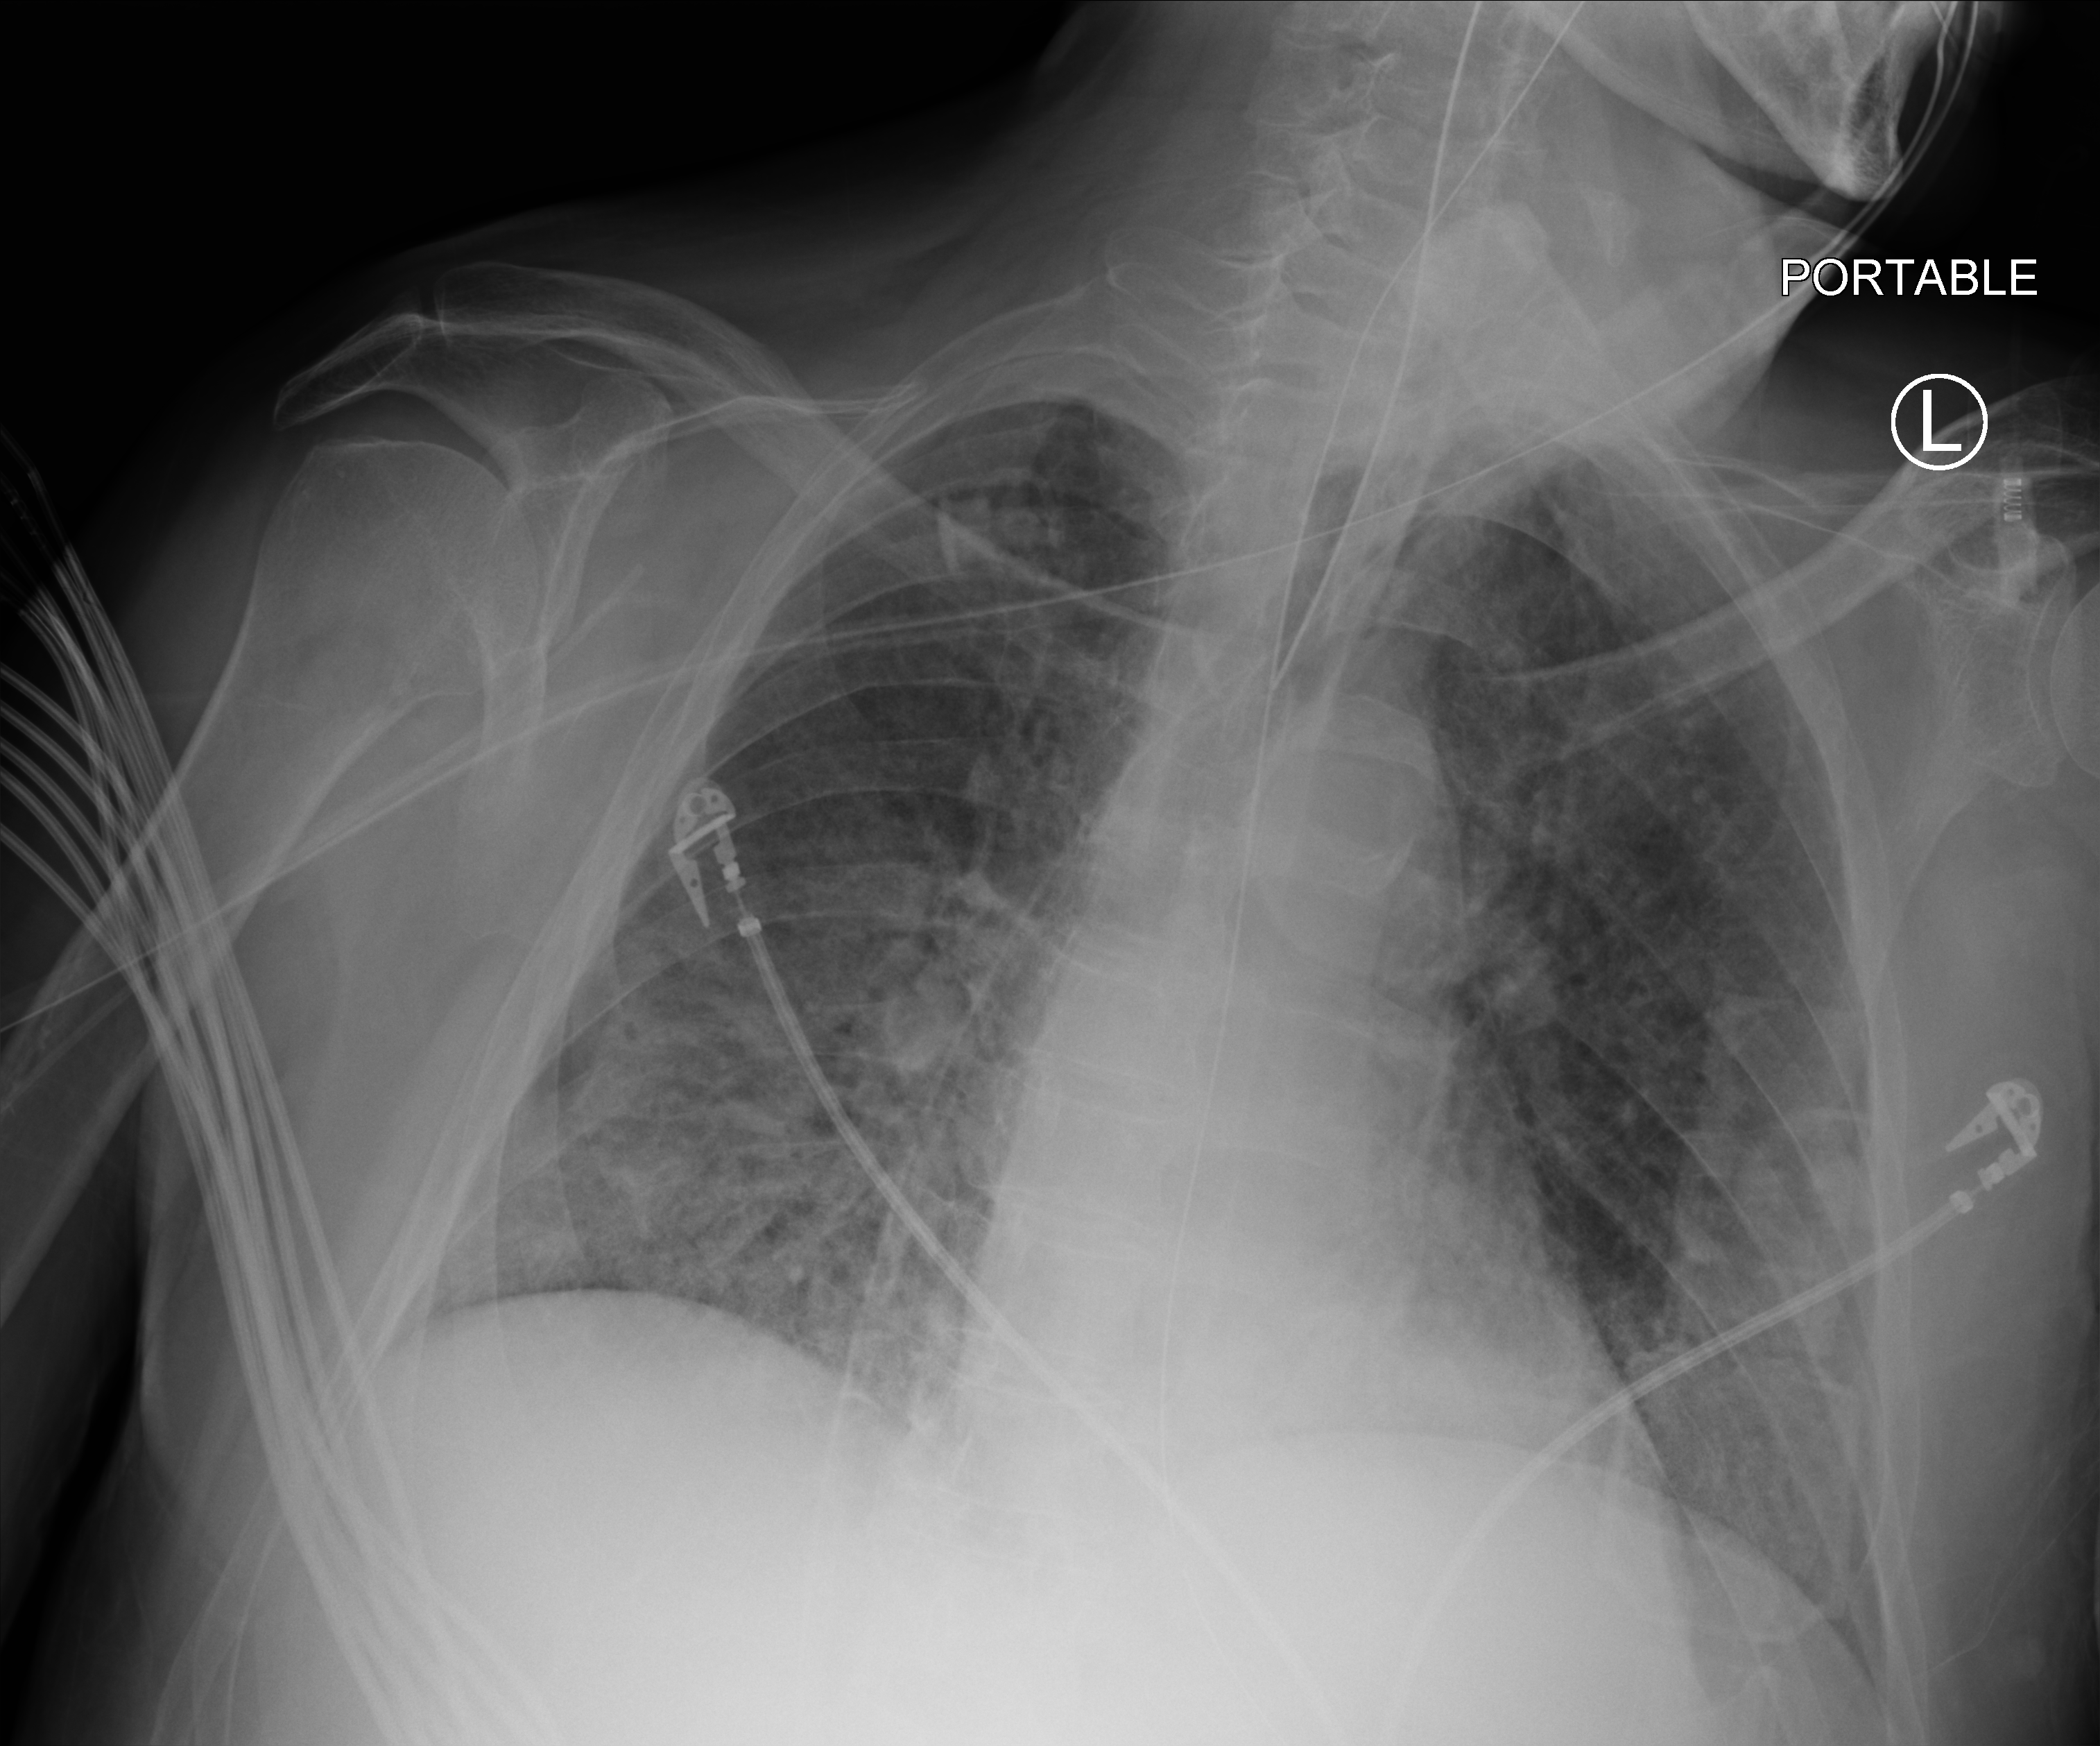
Portable chest radiograph, anteroposterior (AP) projection. Patient hospitalised with COVID-19; male, aged 60–74 years.
From the hospital-stay record, not from the radiograph (when in the stay this image was taken is not recorded):
- admitted to intensive care during this hospital stay: yes